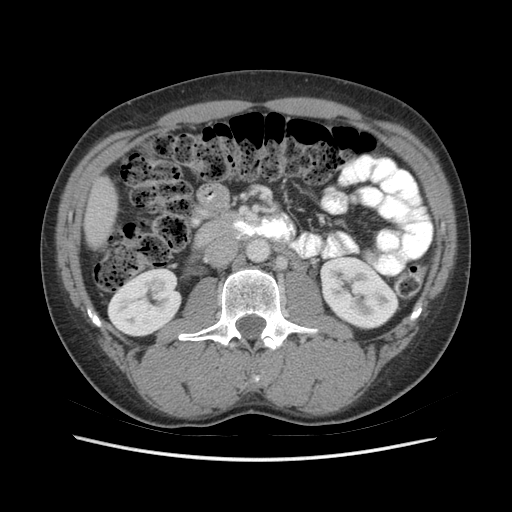
Contrast-enhanced abdominal CT (liver protocol), one axial slice. Position 11 of 73 along the scan axis. Reconstruction kernel STANDARD. 140 kVp. Soft-tissue window (W 400 / L 40 HU). 2.5 mm slice thickness. 512 × 512 image matrix, field of view 360 × 360 mm. Case-level facts recorded for this patient, not image findings: diagnosis: hepatocellular carcinoma (patient treated with transarterial chemoembolisation; whether this scan precedes or follows treatment is not stated here); TNM stage (as recorded): Stage-IIIA.
Outlined on this slice (semi-automatically segmented with operator editing):
- liver parenchyma outside the tumour (the mass and vessels are separate outlines, so this box may not span the whole liver): bounding box <84,176,116,248> (left, top, right, bottom; pixels)